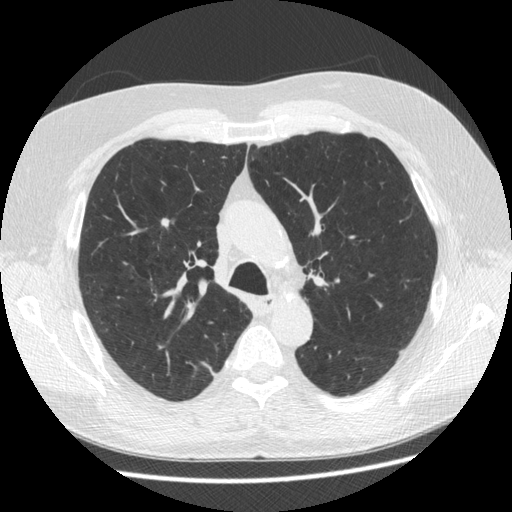
Axial slice from a low-dose chest CT screening exam, third screening round (two years after baseline), lung window (W 1500 / L -600 HU), 1.25 mm slice thickness, 512 × 512 image matrix, field of view 360 × 360 mm. Male, age 63 years at enrolment. Former smoker at enrolment.
• Expert reader's lesion annotation, bounding box (x1, y1, x2, y2) in pixels: (150, 208, 183, 237).
• The screening reader recorded 2 non-calcified nodules or masses ≥4 mm on this exam (right upper lobe, left upper lobe); which of them this box marks is not recorded.
• Later outcome: lung cancer diagnosed 342 days after this screen — adenocarcinoma, NOS, right upper lobe, stage IIA (AJCC 6th edition), 8 mm at pathology.